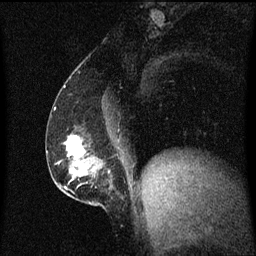
Breast MRI (dynamic contrast-enhanced), one sagittal slice. Position 27 of 60 along the scan axis. Dynamic contrast-enhanced series, image 2 of 3 at this slice position (ordered by acquisition). 1.5 T. TE 4.2 ms, TR 8.4 ms. 2 mm slice thickness. 256 × 256 image matrix, field of view 200 × 200 mm. Female patient, age 52 years. Case-level facts recorded for this patient, not image findings: setting: breast cancer imaged before/during neoadjuvant chemotherapy; receptor status: HER2-positive.
Structures marked on this image (semi-automatically segmented with operator editing):
- analysis volume of interest (the breast-tissue region the enhancement analysis was run in; not a lesion): bounding box <62,134,122,203> (left, top, right, bottom; pixels)
- tumour enhancement mask (voxels above the 70 % enhancement threshold inside the analysis volume of interest): <67,136,86,165>